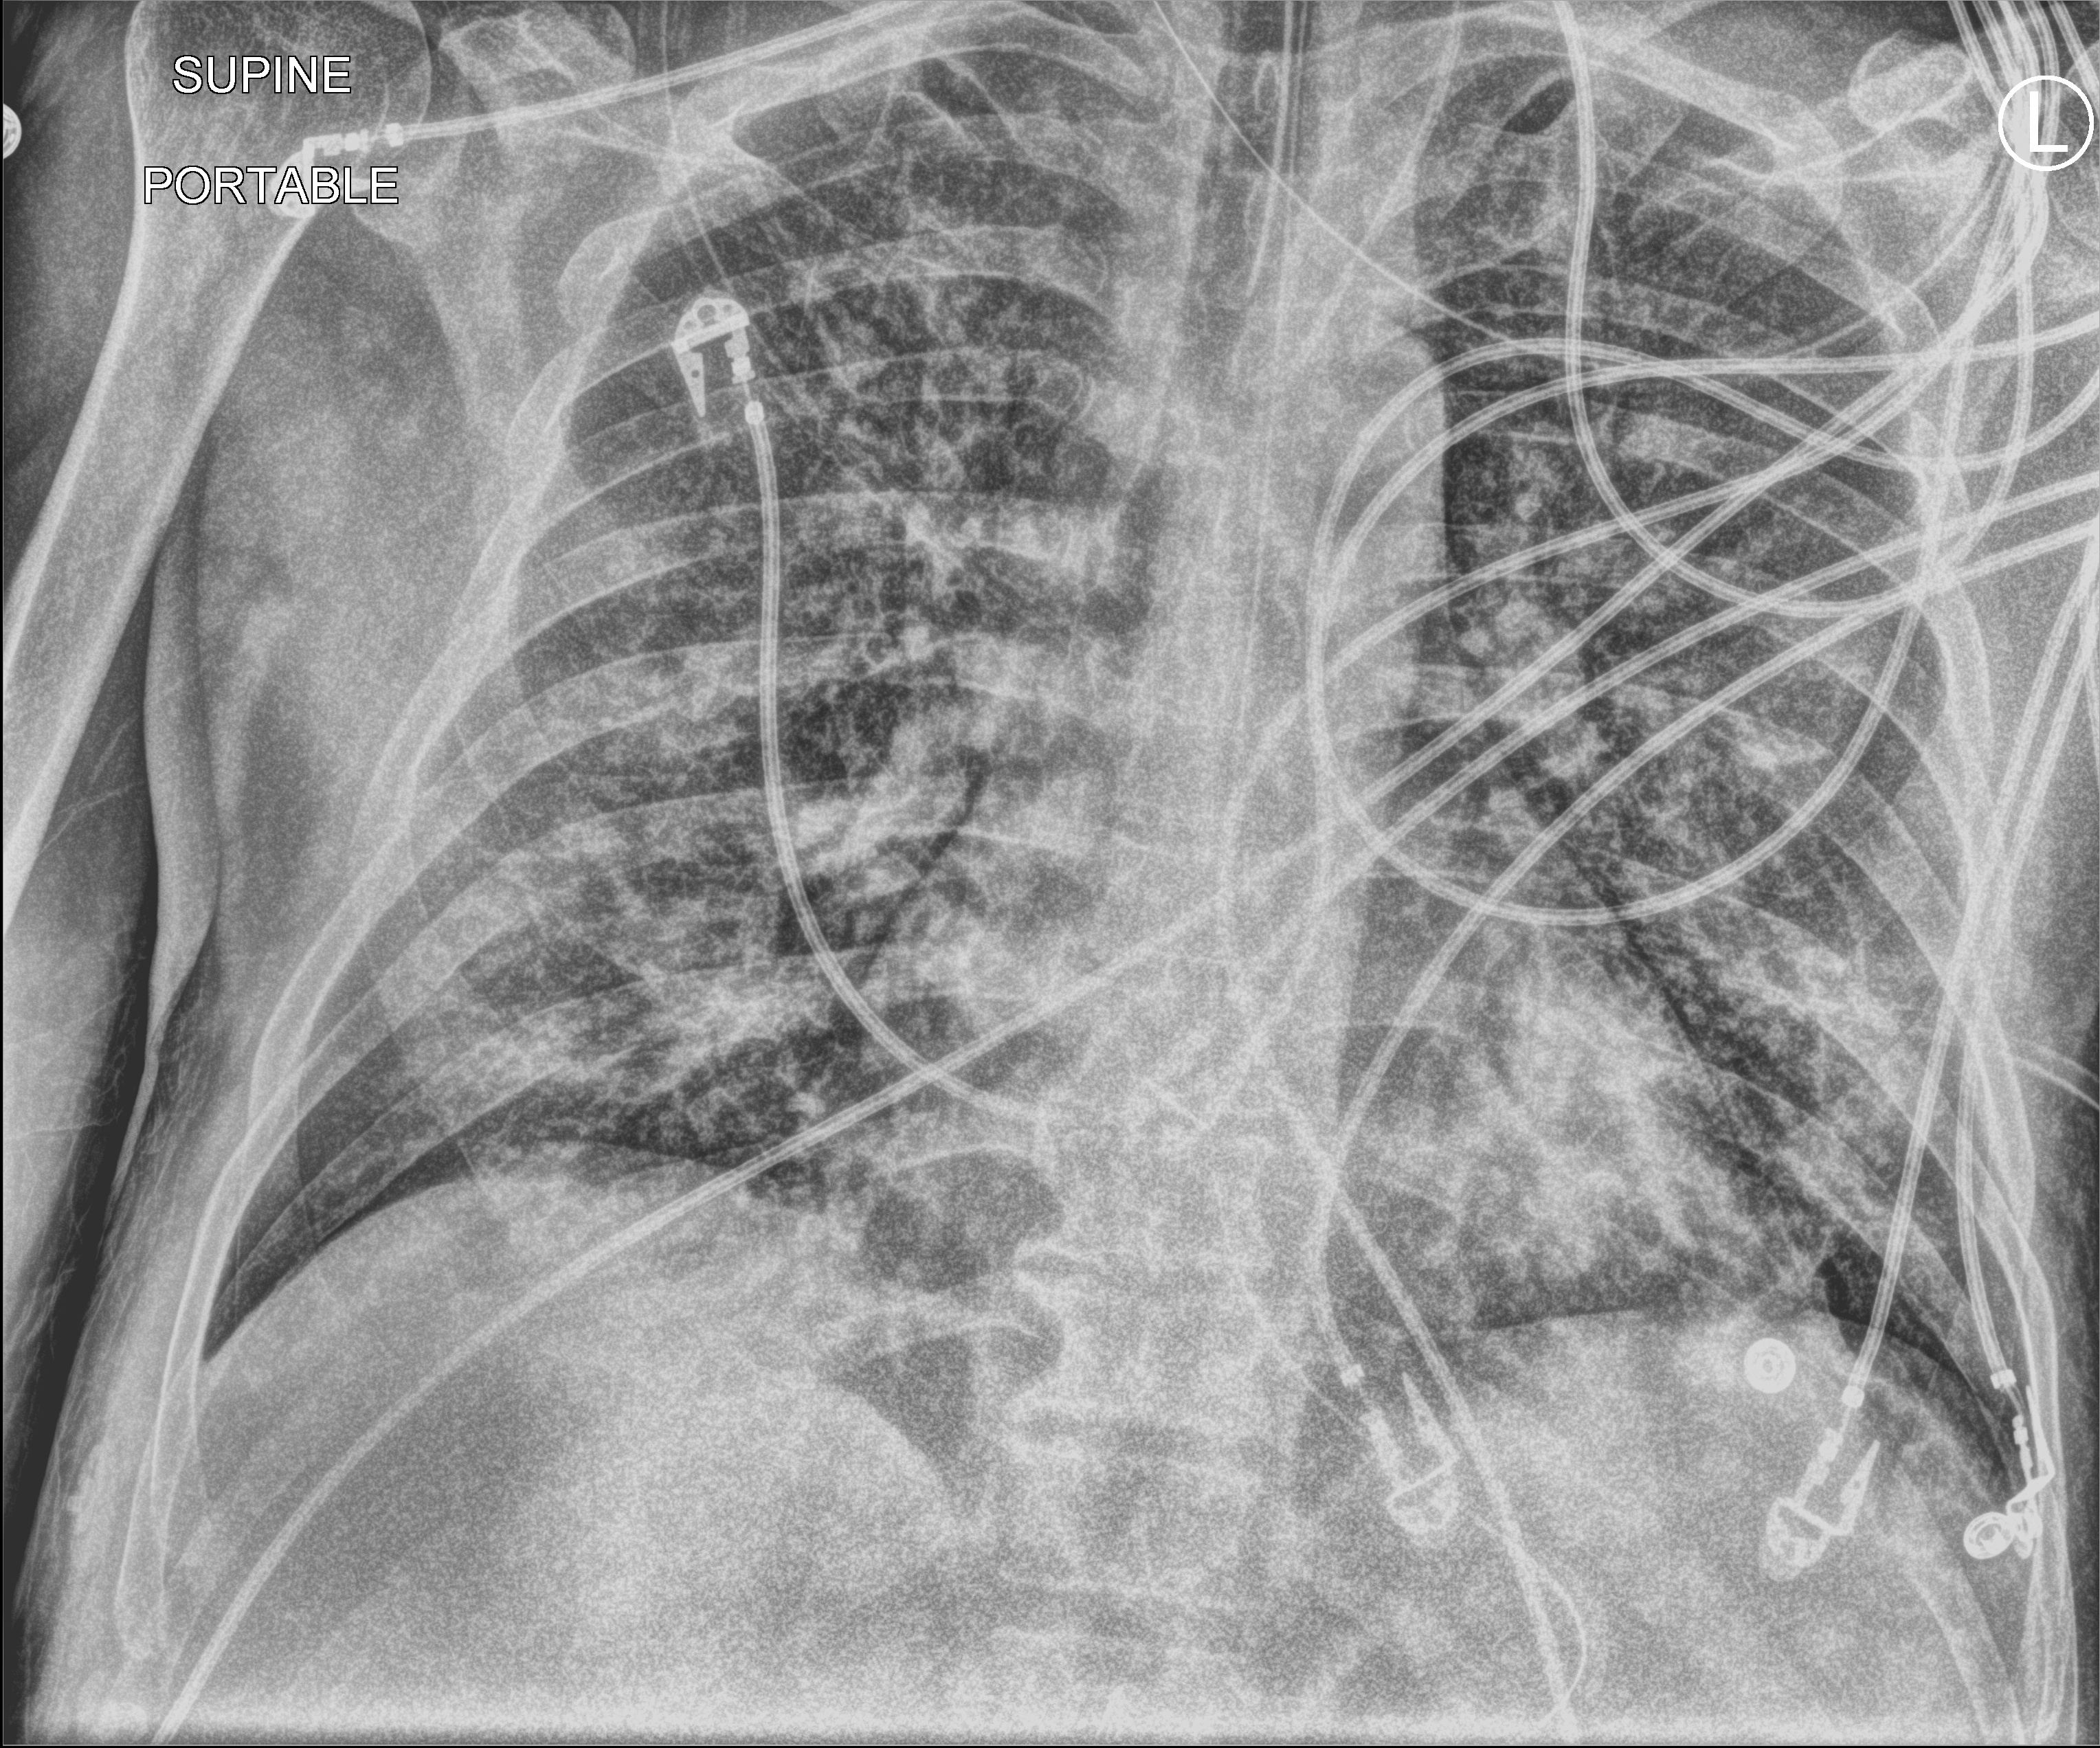
Chest X-ray (portable); anteroposterior (AP) projection. Male patient hospitalised with COVID-19, age 18–59 years.
From the hospital-stay record, not from the radiograph (when in the stay this image was taken is not recorded): admitted to intensive care during this hospital stay: no.